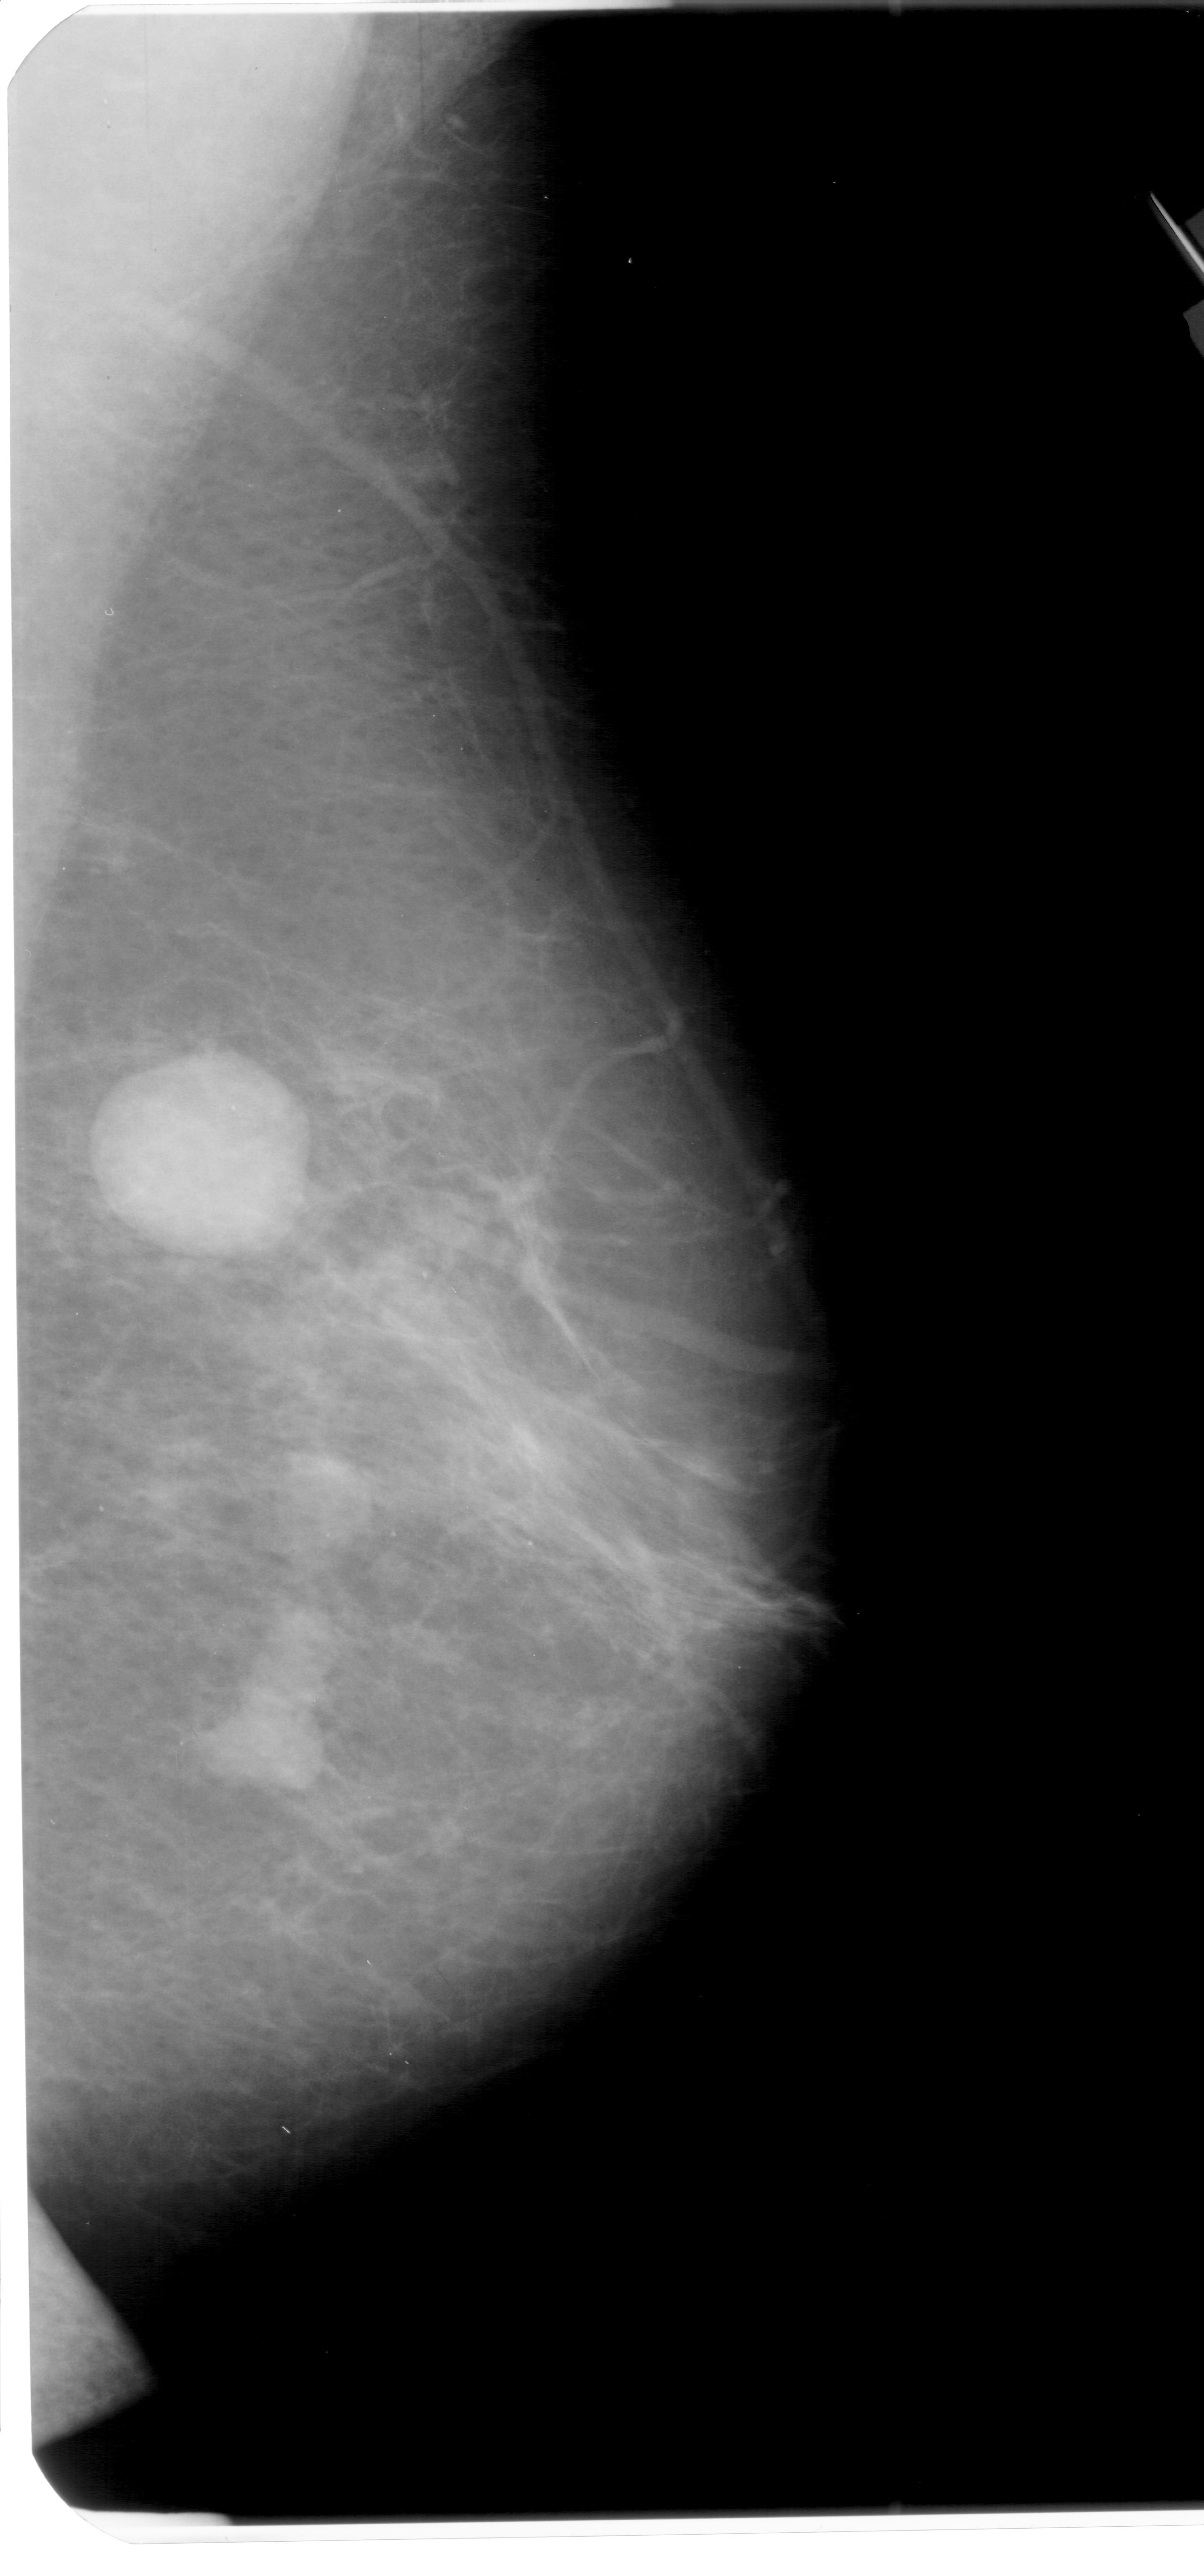
Scanned film-screen mammogram; right breast; mediolateral oblique (MLO) view; BI-RADS breast density category 2 (scale 1–4); 1204 × 2576 image matrix.
Marked abnormalities (boxes around the expert regions of interest):
- Finding 1 of 2: mass, shape oval, margins ill defined; BI-RADS assessment category 4; subtlety rating 5 on a 1 (subtle) to 5 (obvious) scale; pathology (as recorded): malignant: box from (x=107, y=1053) to (x=298, y=1266) px
- Finding 2 of 2: mass, shape oval, margins ill defined; BI-RADS assessment category 4; pathology (as recorded): malignant: (x=192, y=1637)–(x=338, y=1796)